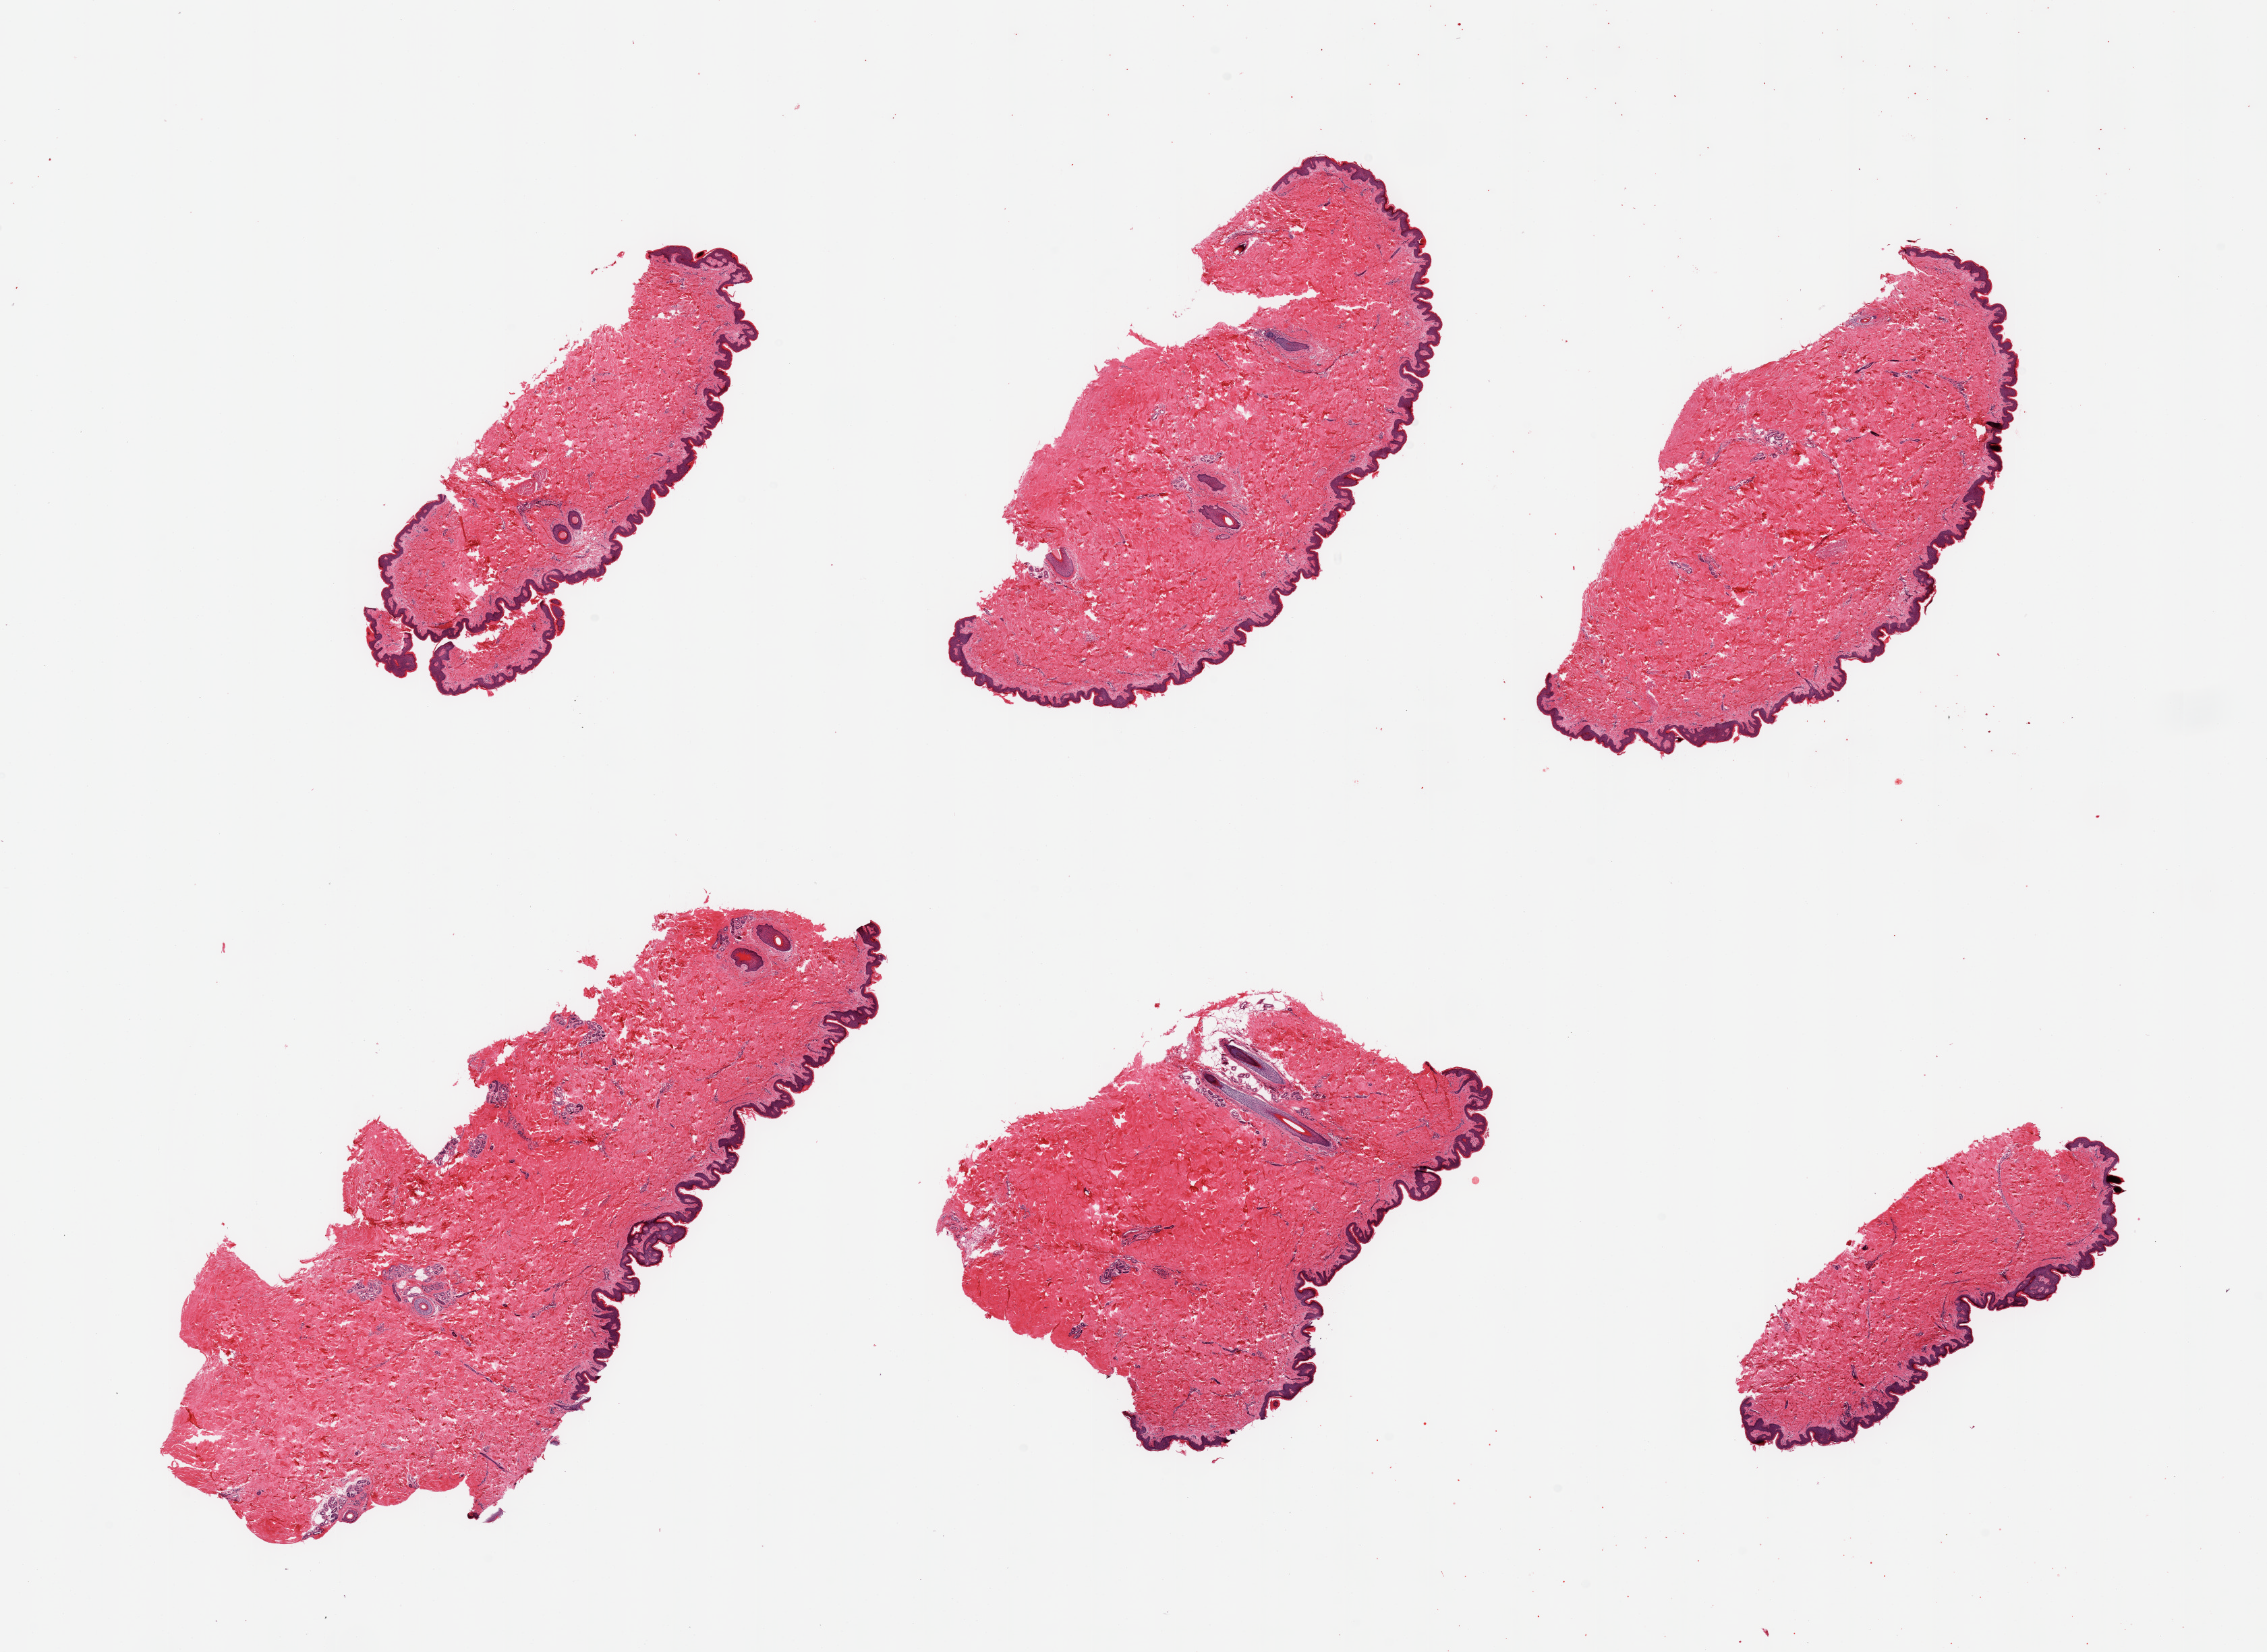
Whole-slide image, hematoxylin and eosin (H&E) stain, whole scanned area (about 26.6 x 19.4 mm, slide scanned at 20x) shown as a low-resolution overview. PAXgene-fixed, paraffin-embedded tissue. Target tissue: skin of suprapubic region. Donor tissue sample. Male donor.
* pathologist's review note for this sample: 6 pieces; well trimmed